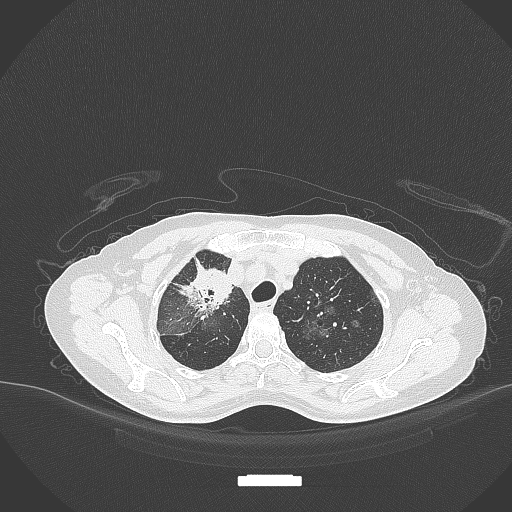
Chest CT, one axial slice. Slice 263 of 284 in the series (ordered by position). Lung window (W 1500 / L -600 HU). 1 mm slice thickness. 512 × 512 image matrix. Patient: female, 59 years. From the clinical record (not read from this slice): clinical TNM (as recorded): T3 N0 M0; histopathological grade: G1.
Outlined on this slice (bounding box drawn by a radiologist):
- lung tumour (recorded histology: adenocarcinoma): box from (x=180, y=264) to (x=238, y=314) px